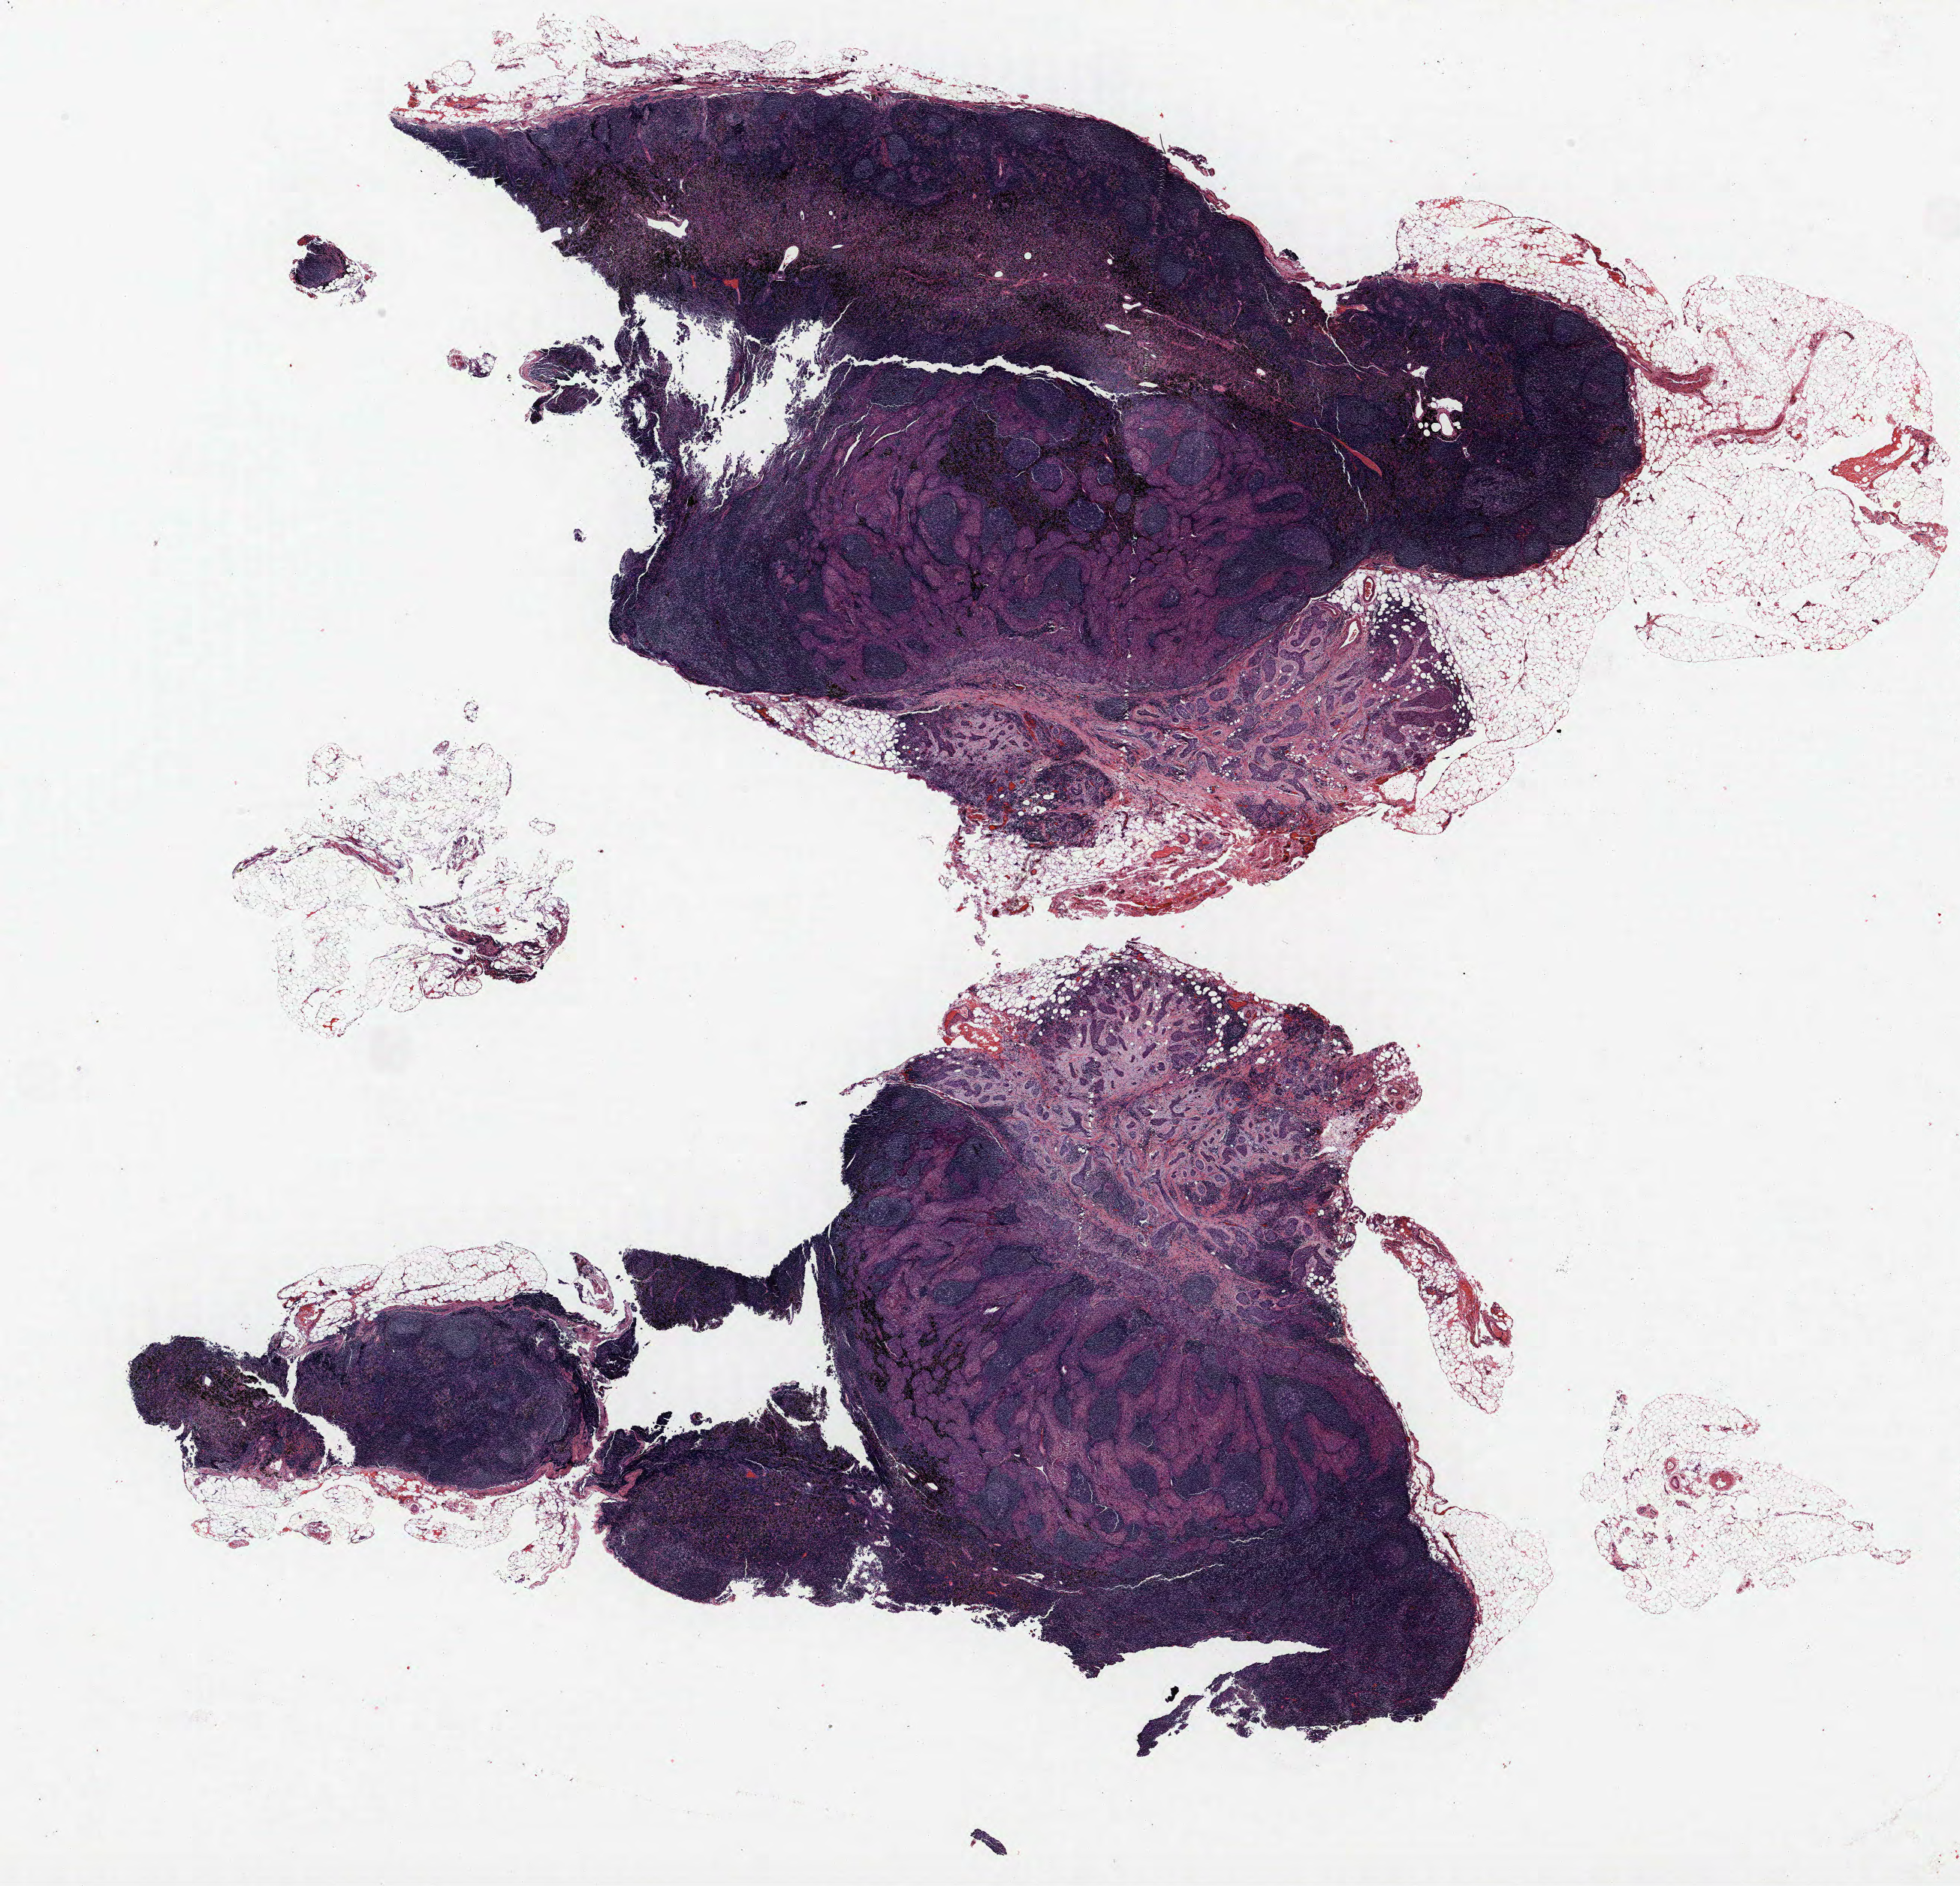
Whole-slide histology image, H&E — whole scanned area (about 20.9 x 20.1 mm, acquisition: 40x scan) shown as a low-resolution overview; formalin-fixed paraffin-embedded (FFPE) section; lung tissue. Male, age 68 at enrolment. Current smoker at enrolment. Grade: moderately differentiated (G2).
Tumour size (pathology): 7 mm. Participant's lung-cancer diagnosis: Squamous cell carcinoma, NOS (ICD-O-3 8070/3). ICD-O-3 topography: upper lobe of lung (C34.1). Stage (AJCC 6th edition): IIIA. Primary tumour location (clinical record): right upper lobe.